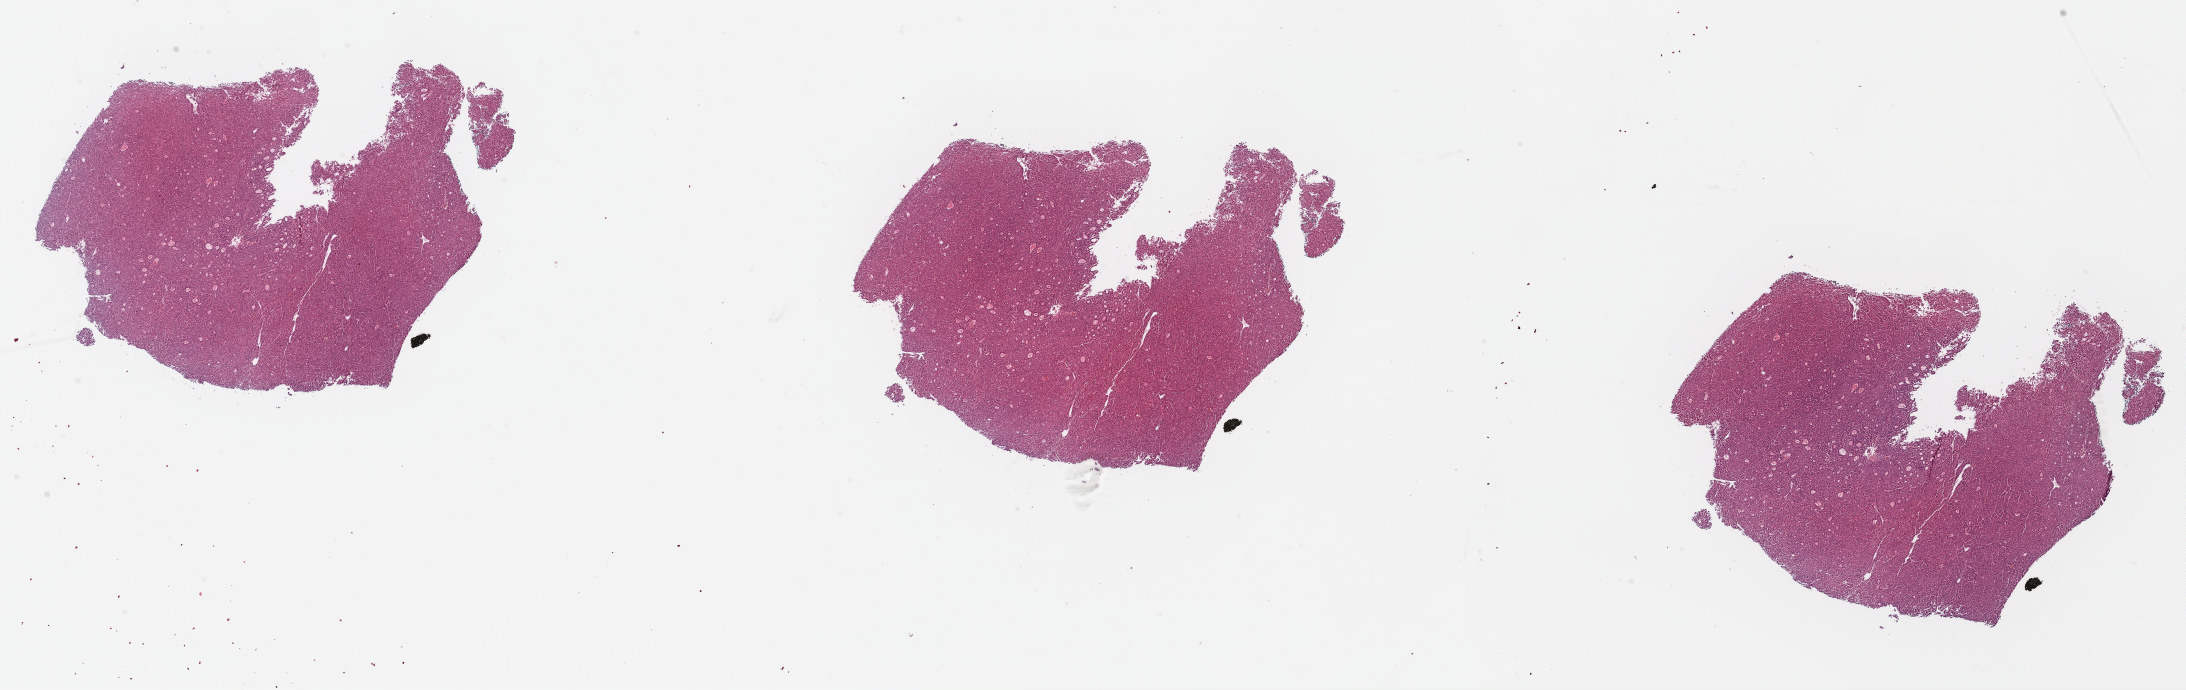
H&E-stained whole-slide image, low-resolution overview of the scanned area, about 34.4 x 10.8 mm; formalin-fixed paraffin-embedded (FFPE) diagnostic section; sample: primary tumour, liver. Patient: male, age at initial diagnosis 62 years. Histologic grade: G1 (well differentiated).
- histologic diagnosis: Hepatocellular carcinoma, NOS
- AJCC pathologic stage: I